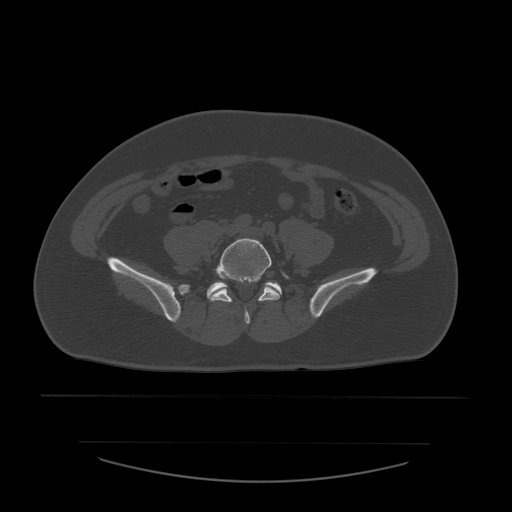
CT including the spine, one axial slice. Position 115 of 532 along the scan axis. Bone window (W 1800 / L 400 HU). 1.25 mm slice thickness. 512 × 512 image matrix. Patient age 44 years. Case-level facts recorded for this patient, not image findings: primary cancer: soft tissue sarcoma.
Outlined on this slice (semi-automatically segmented with operator editing):
- L5 vertebra: box from (x=208, y=238) to (x=289, y=325) px